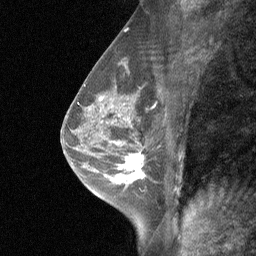
Breast MRI (dynamic contrast-enhanced), one sagittal slice. Slice 37 of 64 in the series (ordered by position). Dynamic contrast-enhanced study with each time point stored as its own series, time point 2 of 3 at this slice position (early post-contrast, ordered by acquisition time). 1.5 T. TE 4.8 ms, TR 27 ms. 2 mm slice thickness. 256 × 256 image matrix, field of view 180 × 180 mm. Patient: female, 47 years. Case-level facts recorded for this patient, not image findings: setting: breast cancer imaged before/during neoadjuvant chemotherapy; receptor status: HR-positive, HER2-negative.
Annotated regions visible in this slice (semi-automatic segmentation, software-assisted and operator-edited):
- analysis volume of interest (the breast-tissue region the enhancement analysis was run in; not a lesion): bounding box <104,138,159,198> (left, top, right, bottom; pixels)
- tumour enhancement mask (voxels above the 90 % enhancement threshold inside the analysis volume of interest): <116,153,146,184>